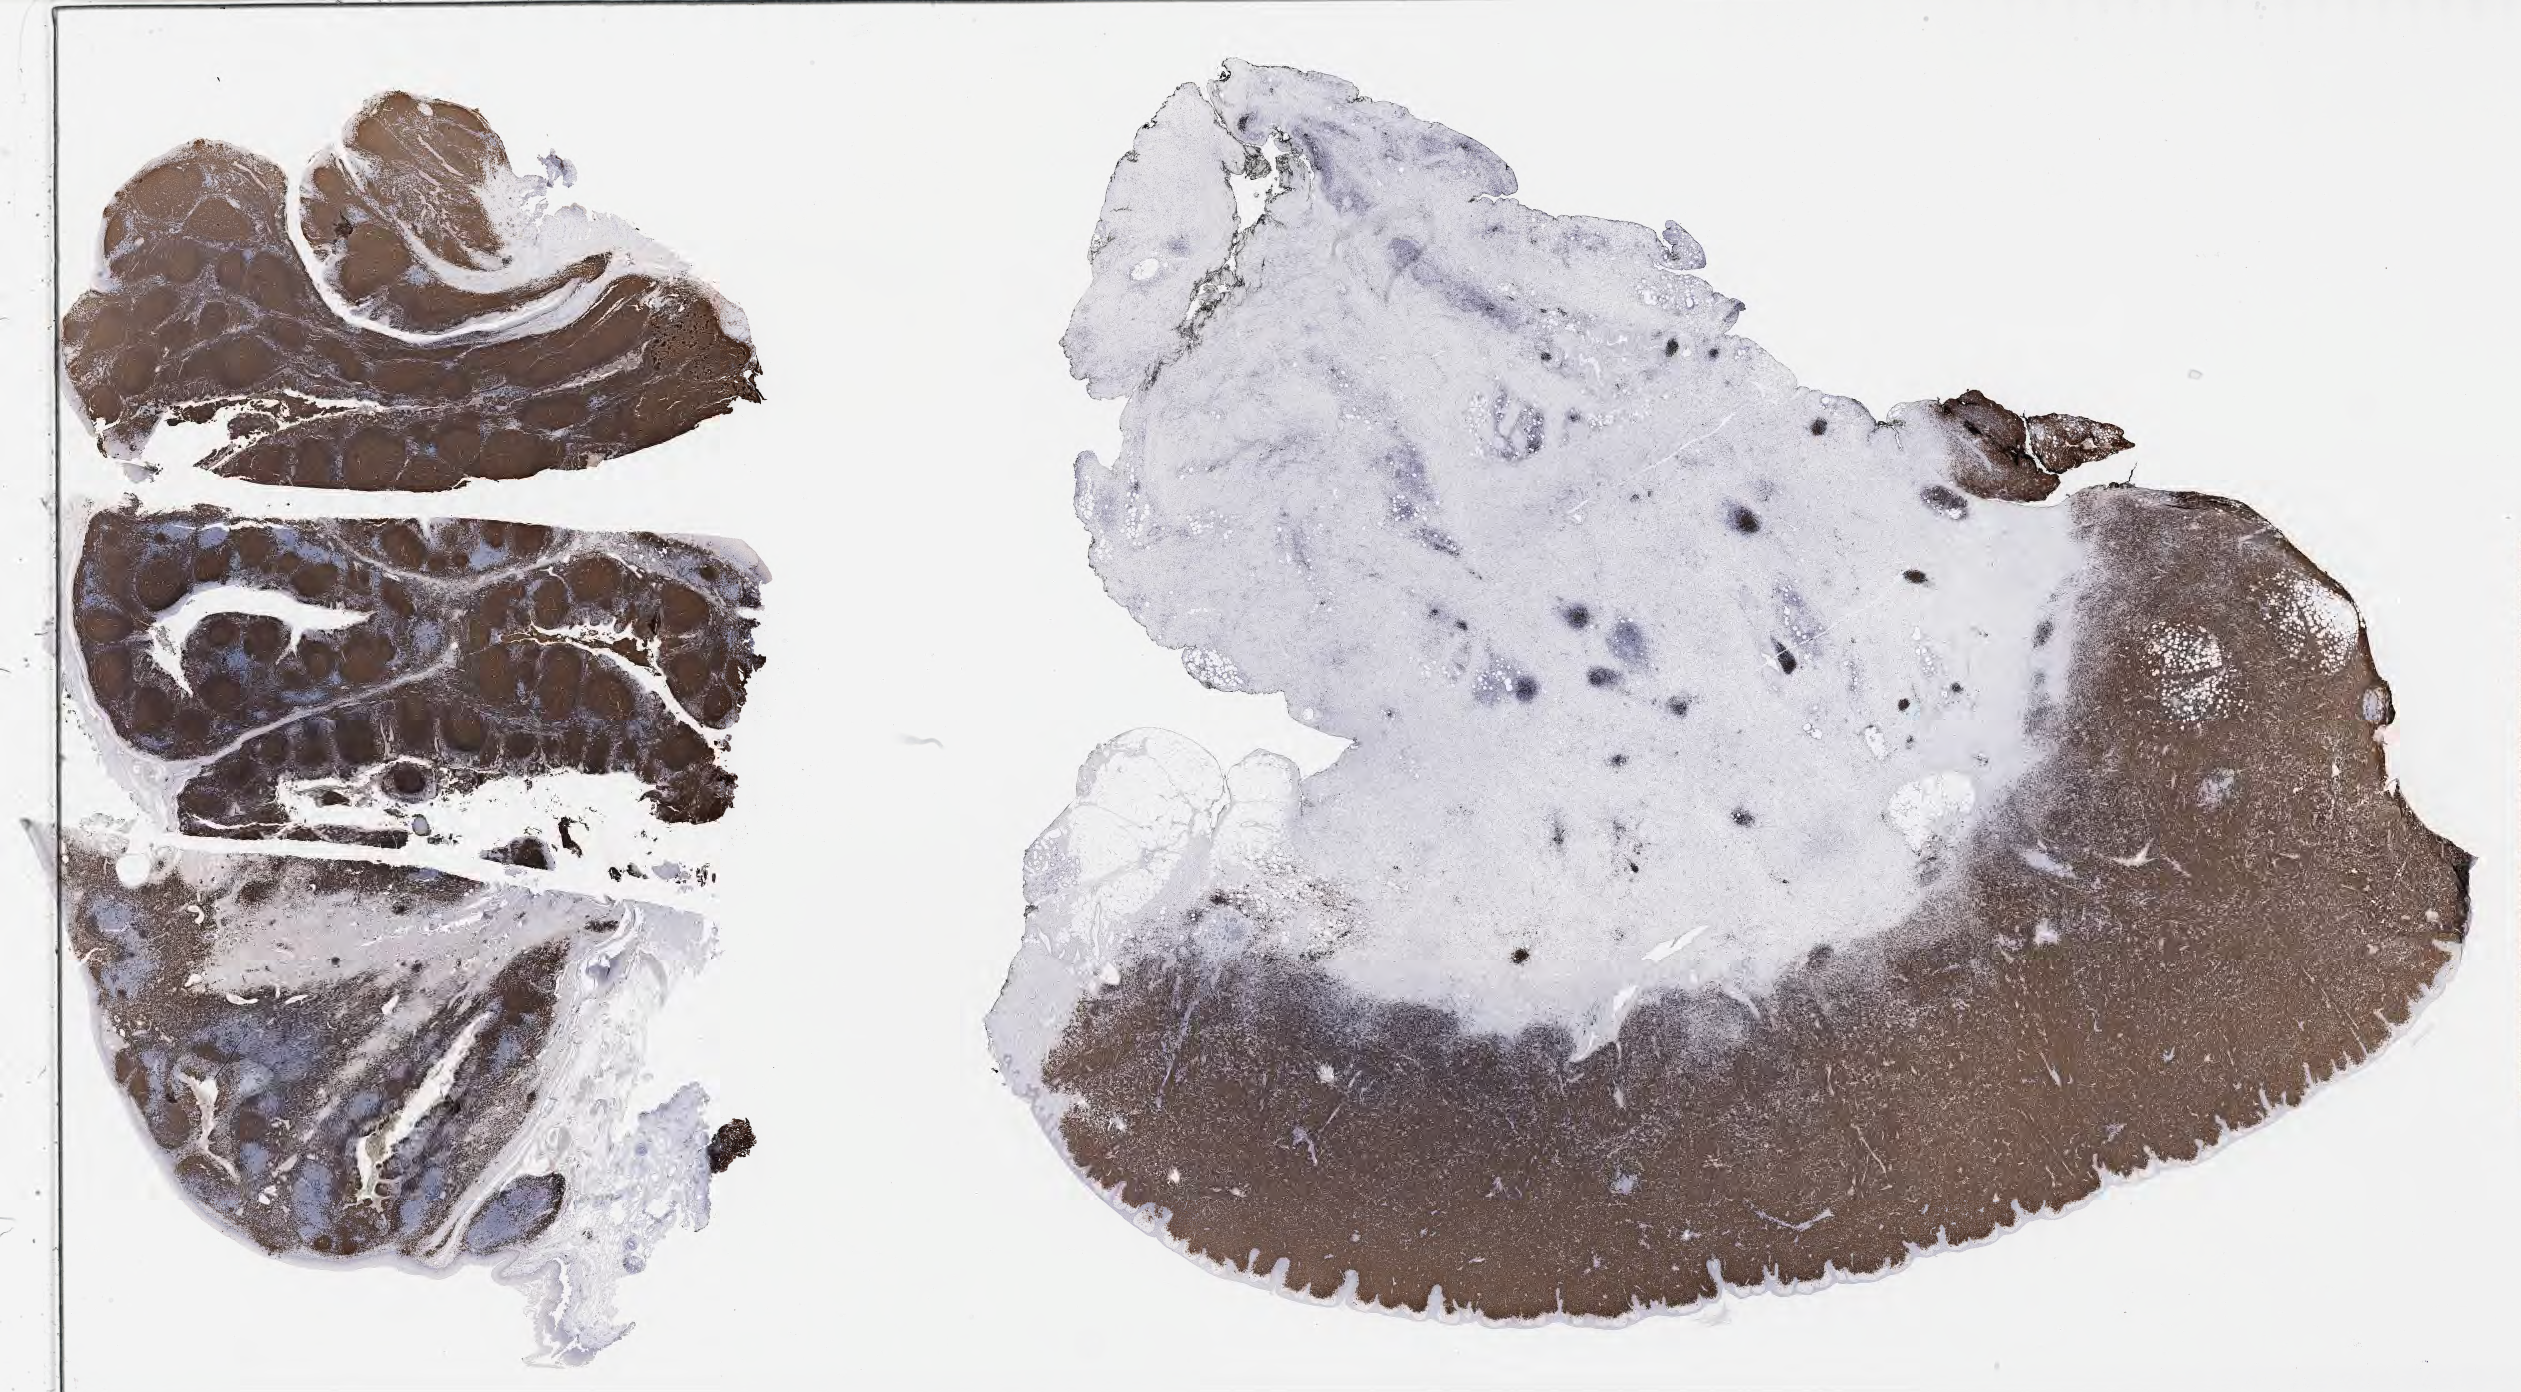
Immunohistochemistry (IHC) whole-slide image stained for CD20, low-resolution overview of the scanned area, about 40.7 x 22.5 mm, specimen: tumor tissue, site: lymph node. Patient: male, 52 years old.
- histologic diagnosis: Diffuse large B-cell lymphoma, NOS